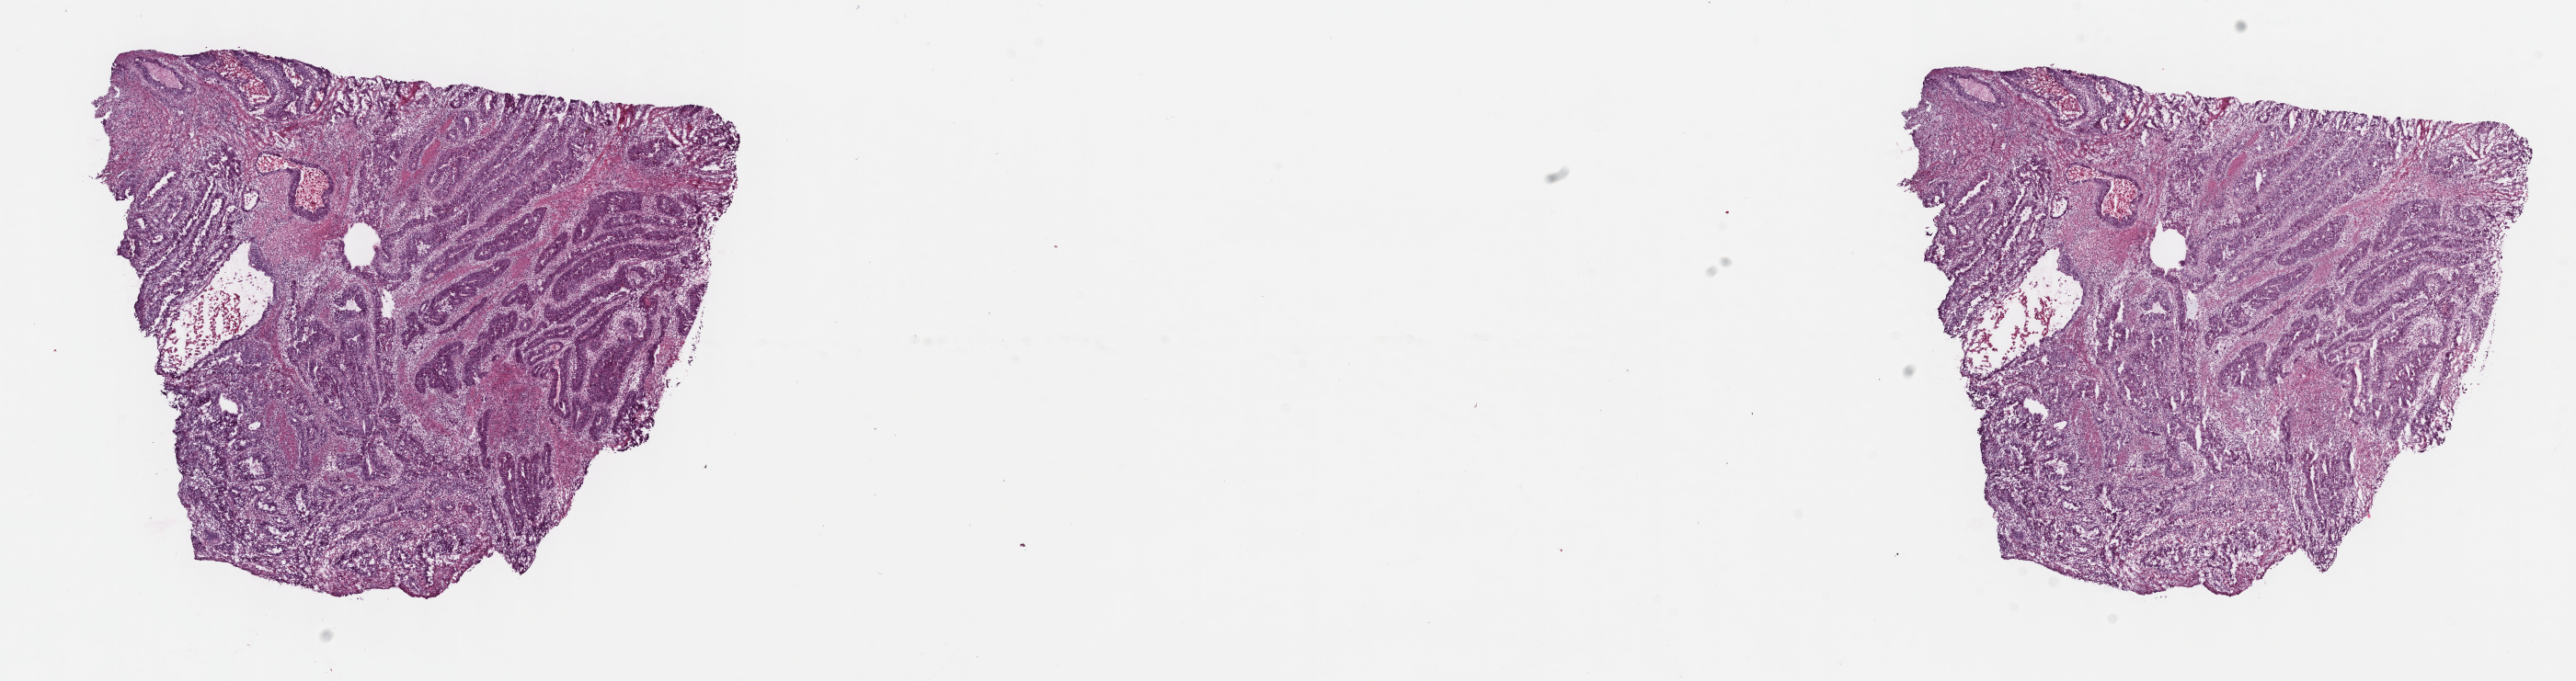
Whole-slide histology image, H&E-stained, shown as a low-resolution overview of the whole scanned area (about 22.7 x 6.0 mm, from a 40x scan). Composition of this section per pathologist review: tumour cells 60%, tumour nuclei 60%, normal cells 15%, stromal cells 20%, necrosis 5%. Inflammatory infiltration, as recorded: lymphocyte infiltration 10%, monocyte infiltration 0%, neutrophil infiltration 0%.
Specimen: frozen section from the top of the tissue portion; colon, primary tumour sample.